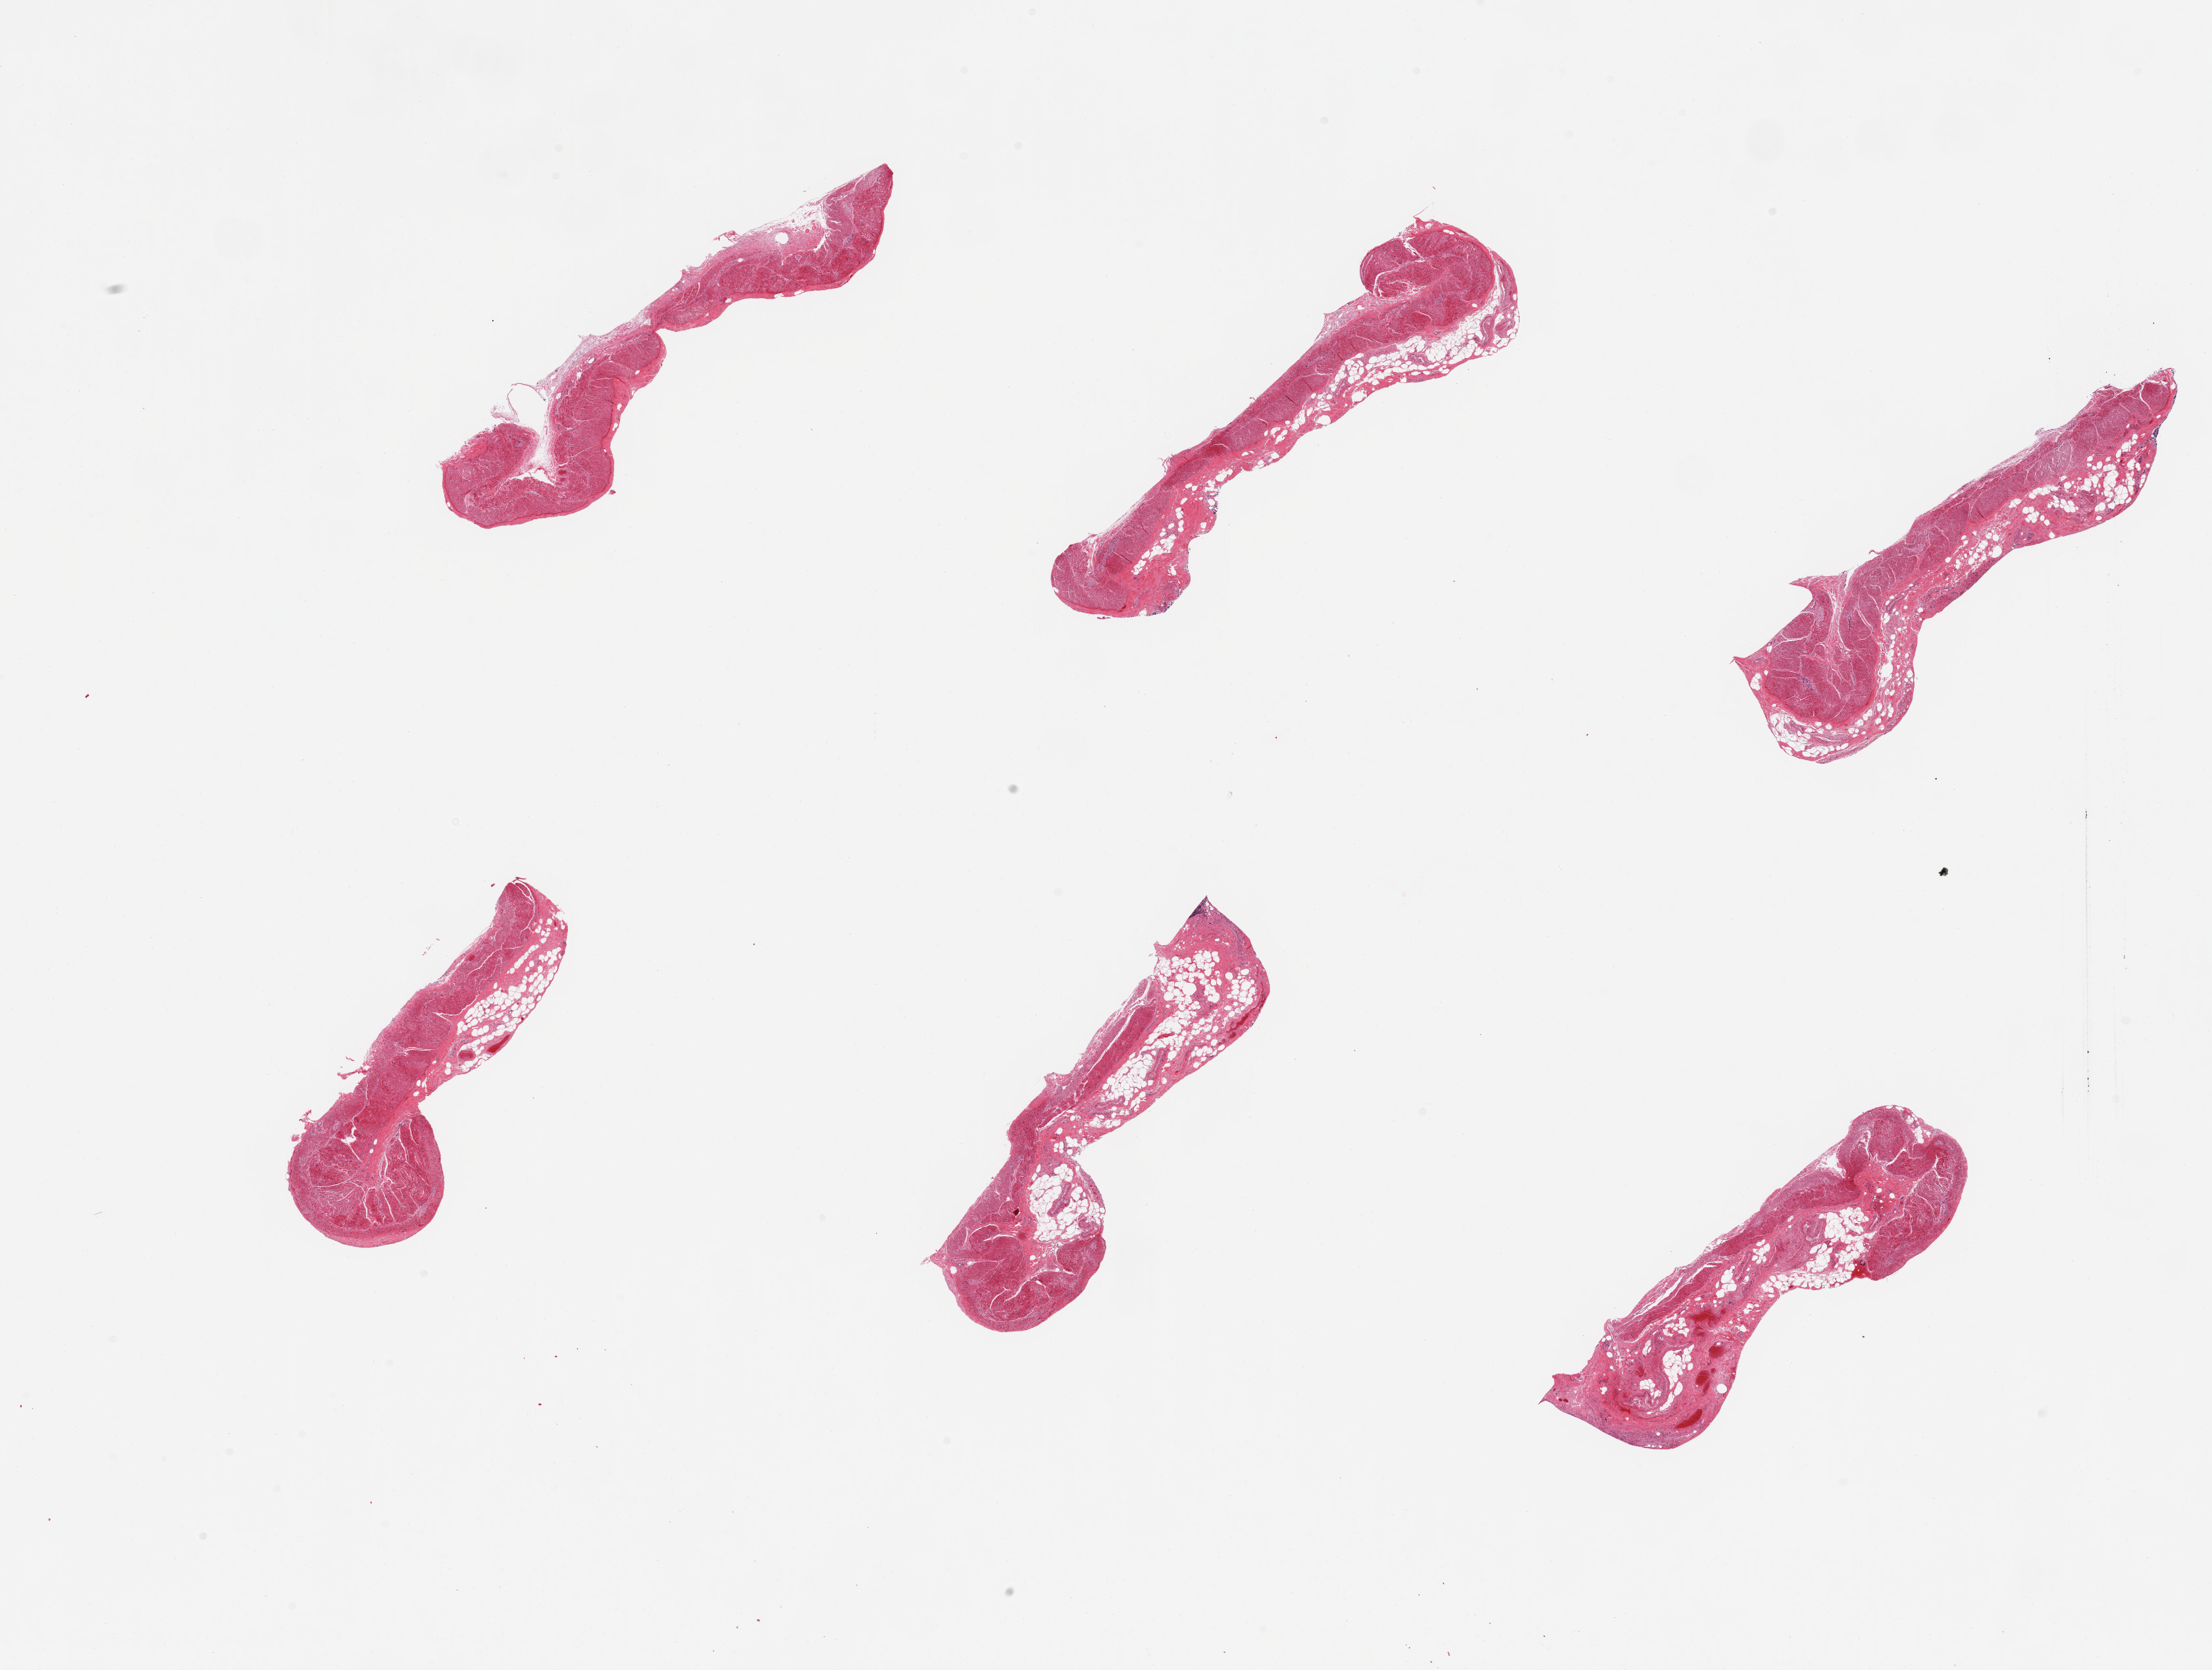
H&E whole-slide image — low-resolution overview of the scanned area, about 26.6 x 20.1 mm. PAXgene-fixed paraffin-embedded (PFPE) section. Section of sigmoid colon (target tissue). Donor tissue sample. Male donor.
Reviewer comment on this tissue sample: 6 pieces; too much submucosal fat, up to 75%.